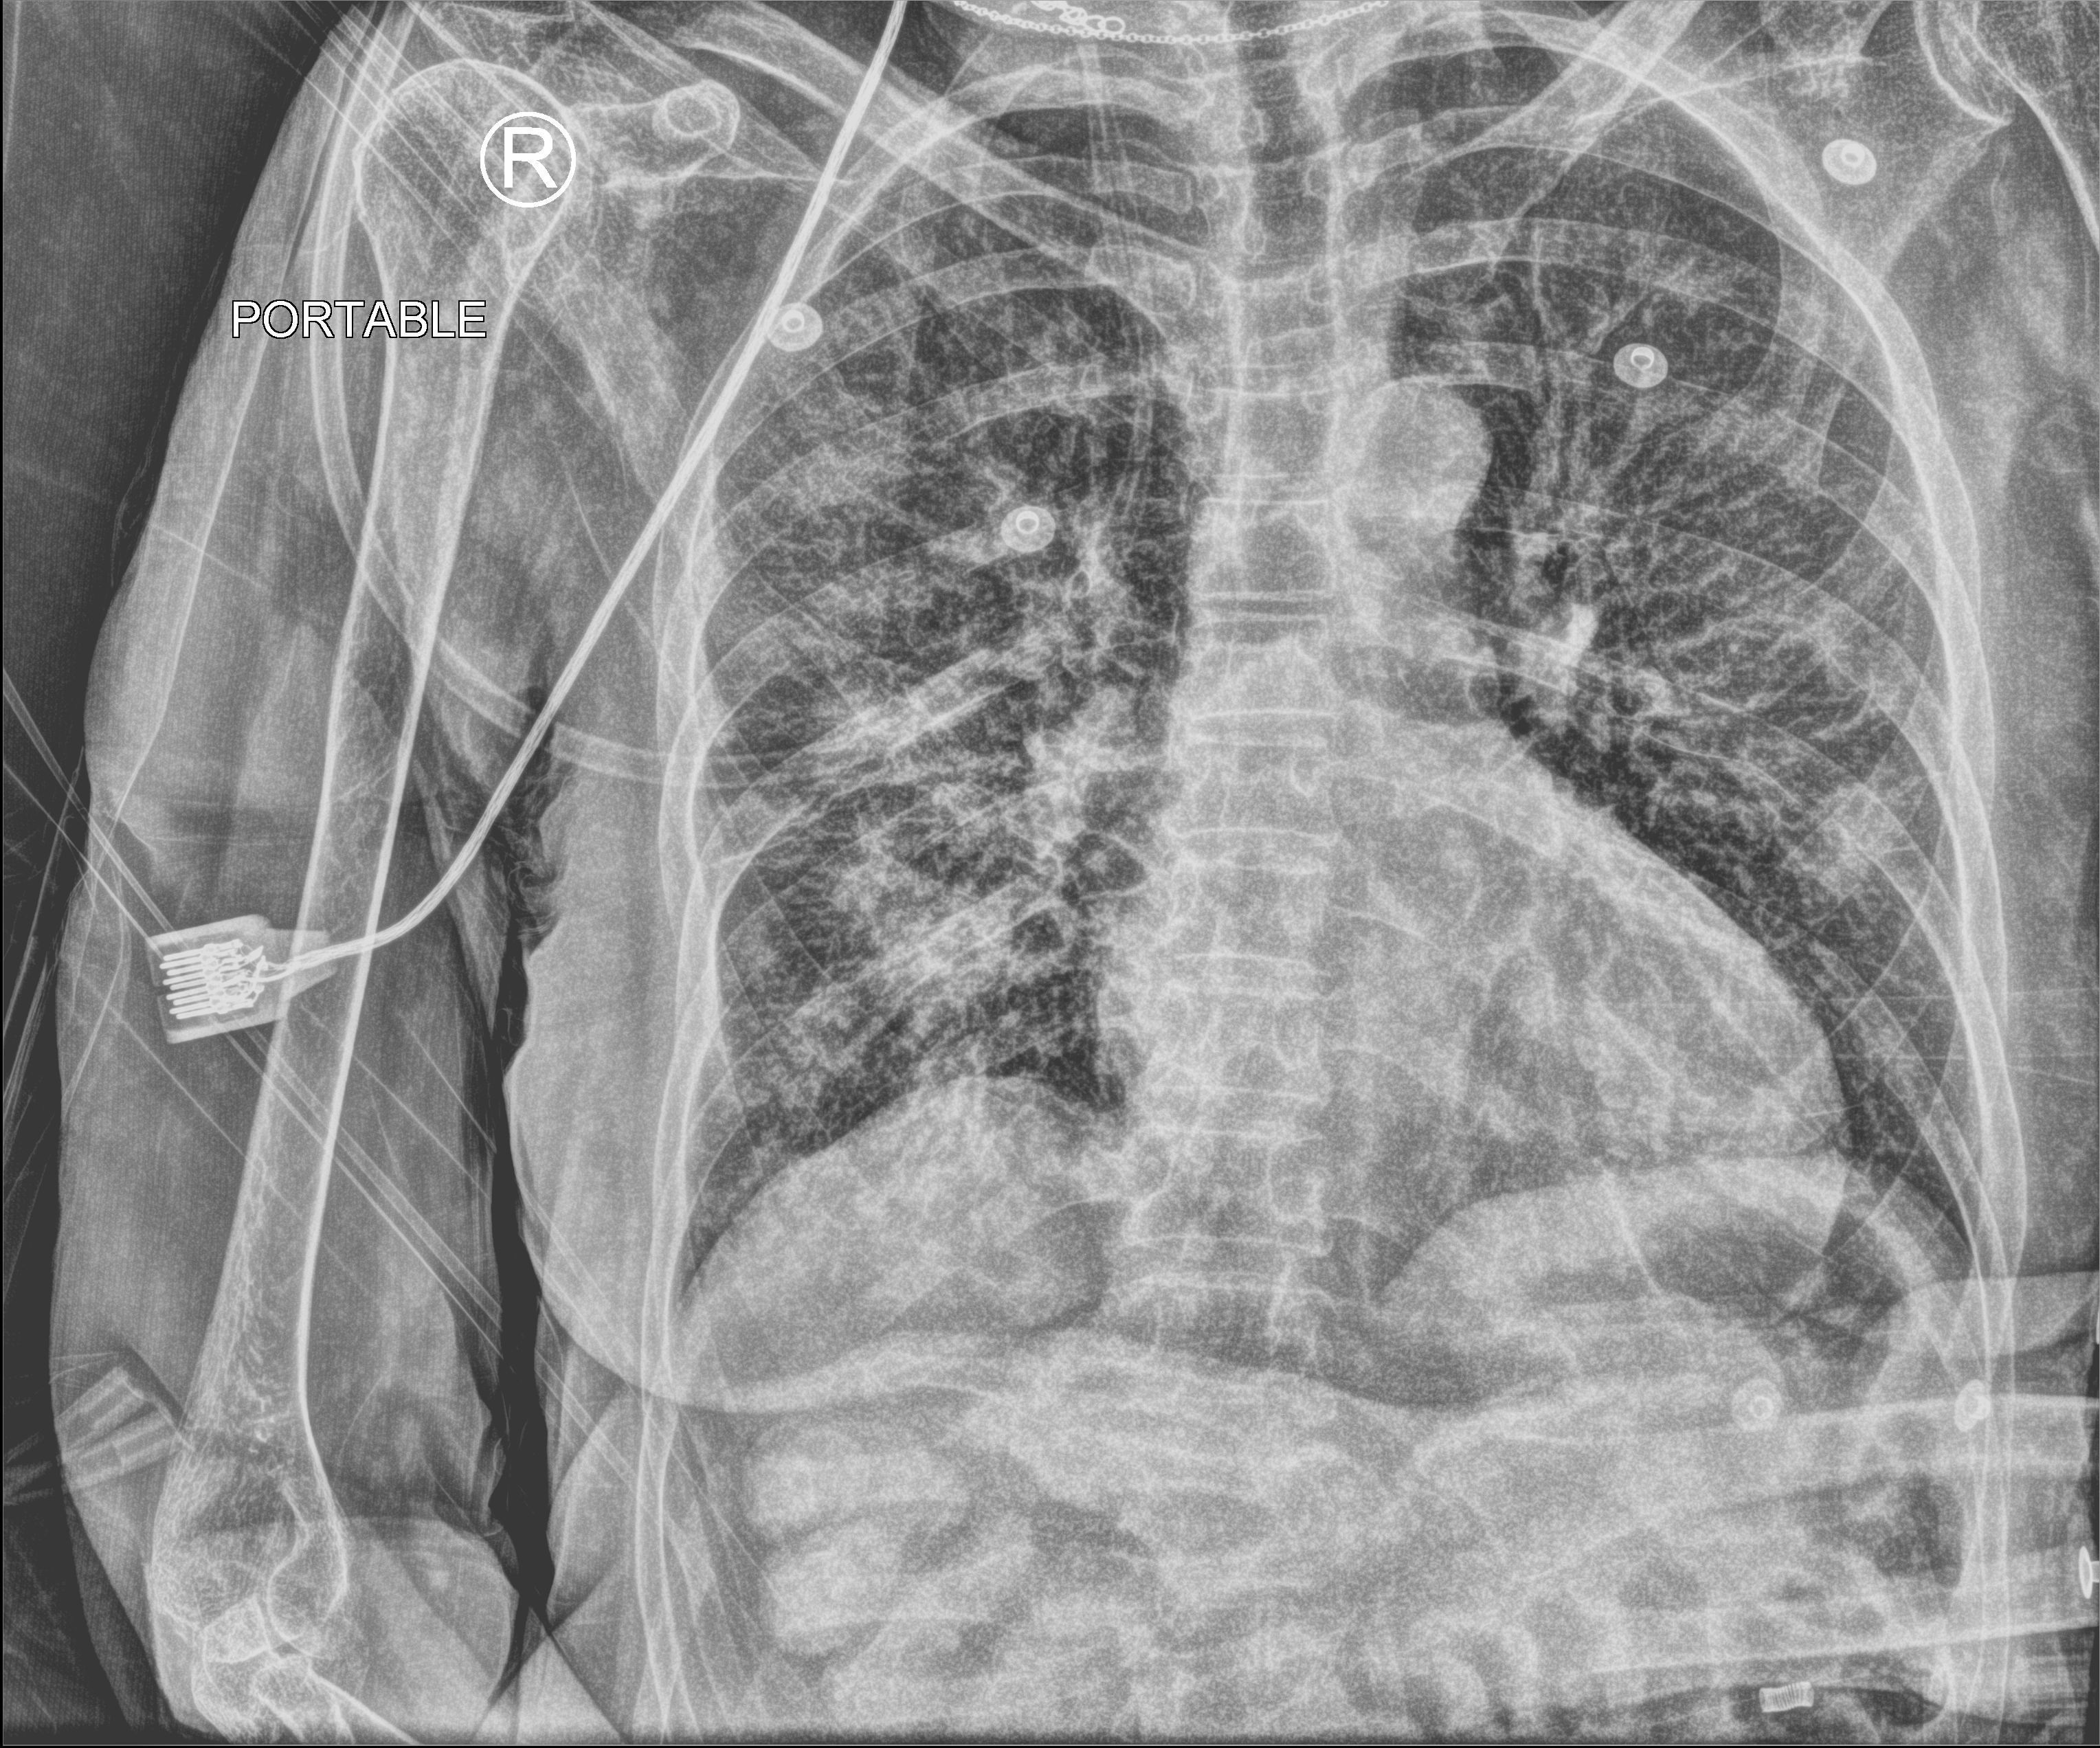
Portable chest radiograph, anteroposterior (AP) projection. Female patient hospitalised with COVID-19, age 75–90 years.
Hospital-stay facts (about this admission, not read from this image; timing relative to this image not recorded): smoking status (admission record): never; COPD (admission record): no.